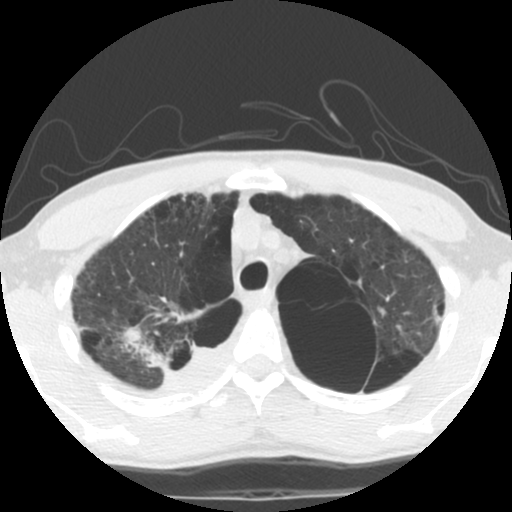
Low-dose screening chest CT, axial slice. Second annual screen. Lung window (W 1500 / L -600 HU). 2.5 mm slice thickness. Standard (soft-tissue) reconstruction kernel (STANDARD). 512 × 512 image matrix, field of view 295 × 295 mm. Male, age 62 years at enrolment. Current smoker at enrolment.
• Expert reader's lesion annotation, bounding box (x1, y1, x2, y2) in pixels: (124, 320, 215, 393).
• The exam's reader record, not a measurement of the box and not confirmed to be the same lesion: non-calcified nodule or mass ≥4 mm, 35 × 25 mm, soft tissue attenuation.
• Later outcome: lung cancer diagnosed 14 days after this screen — non-small cell carcinoma, right upper lobe, poorly differentiated (G3), stage IA (AJCC 6th edition), 70 mm at pathology.